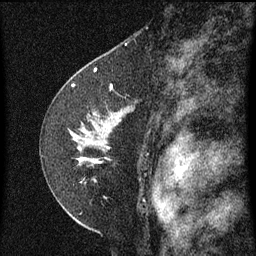
Breast MRI (dynamic contrast-enhanced), one sagittal slice; position 42 of 60 along the scan axis; dynamic contrast-enhanced series, image 2 of 3 at this slice position (ordered by acquisition); 1.5 T; TE 4.2 ms, TR 8 ms; 2 mm slice thickness; 256 × 256 image matrix, field of view 180 × 180 mm. Patient: female, 47 years.
Structures marked on this image (semi-automatic segmentation, software-assisted and operator-edited):
- analysis volume of interest (the breast-tissue region the enhancement analysis was run in; not a lesion): bounding box (x1, y1, x2, y2) in pixels: (48, 84, 141, 199)
- tumour enhancement mask (voxels above the 70 % enhancement threshold inside the analysis volume of interest): (74, 84, 101, 163)